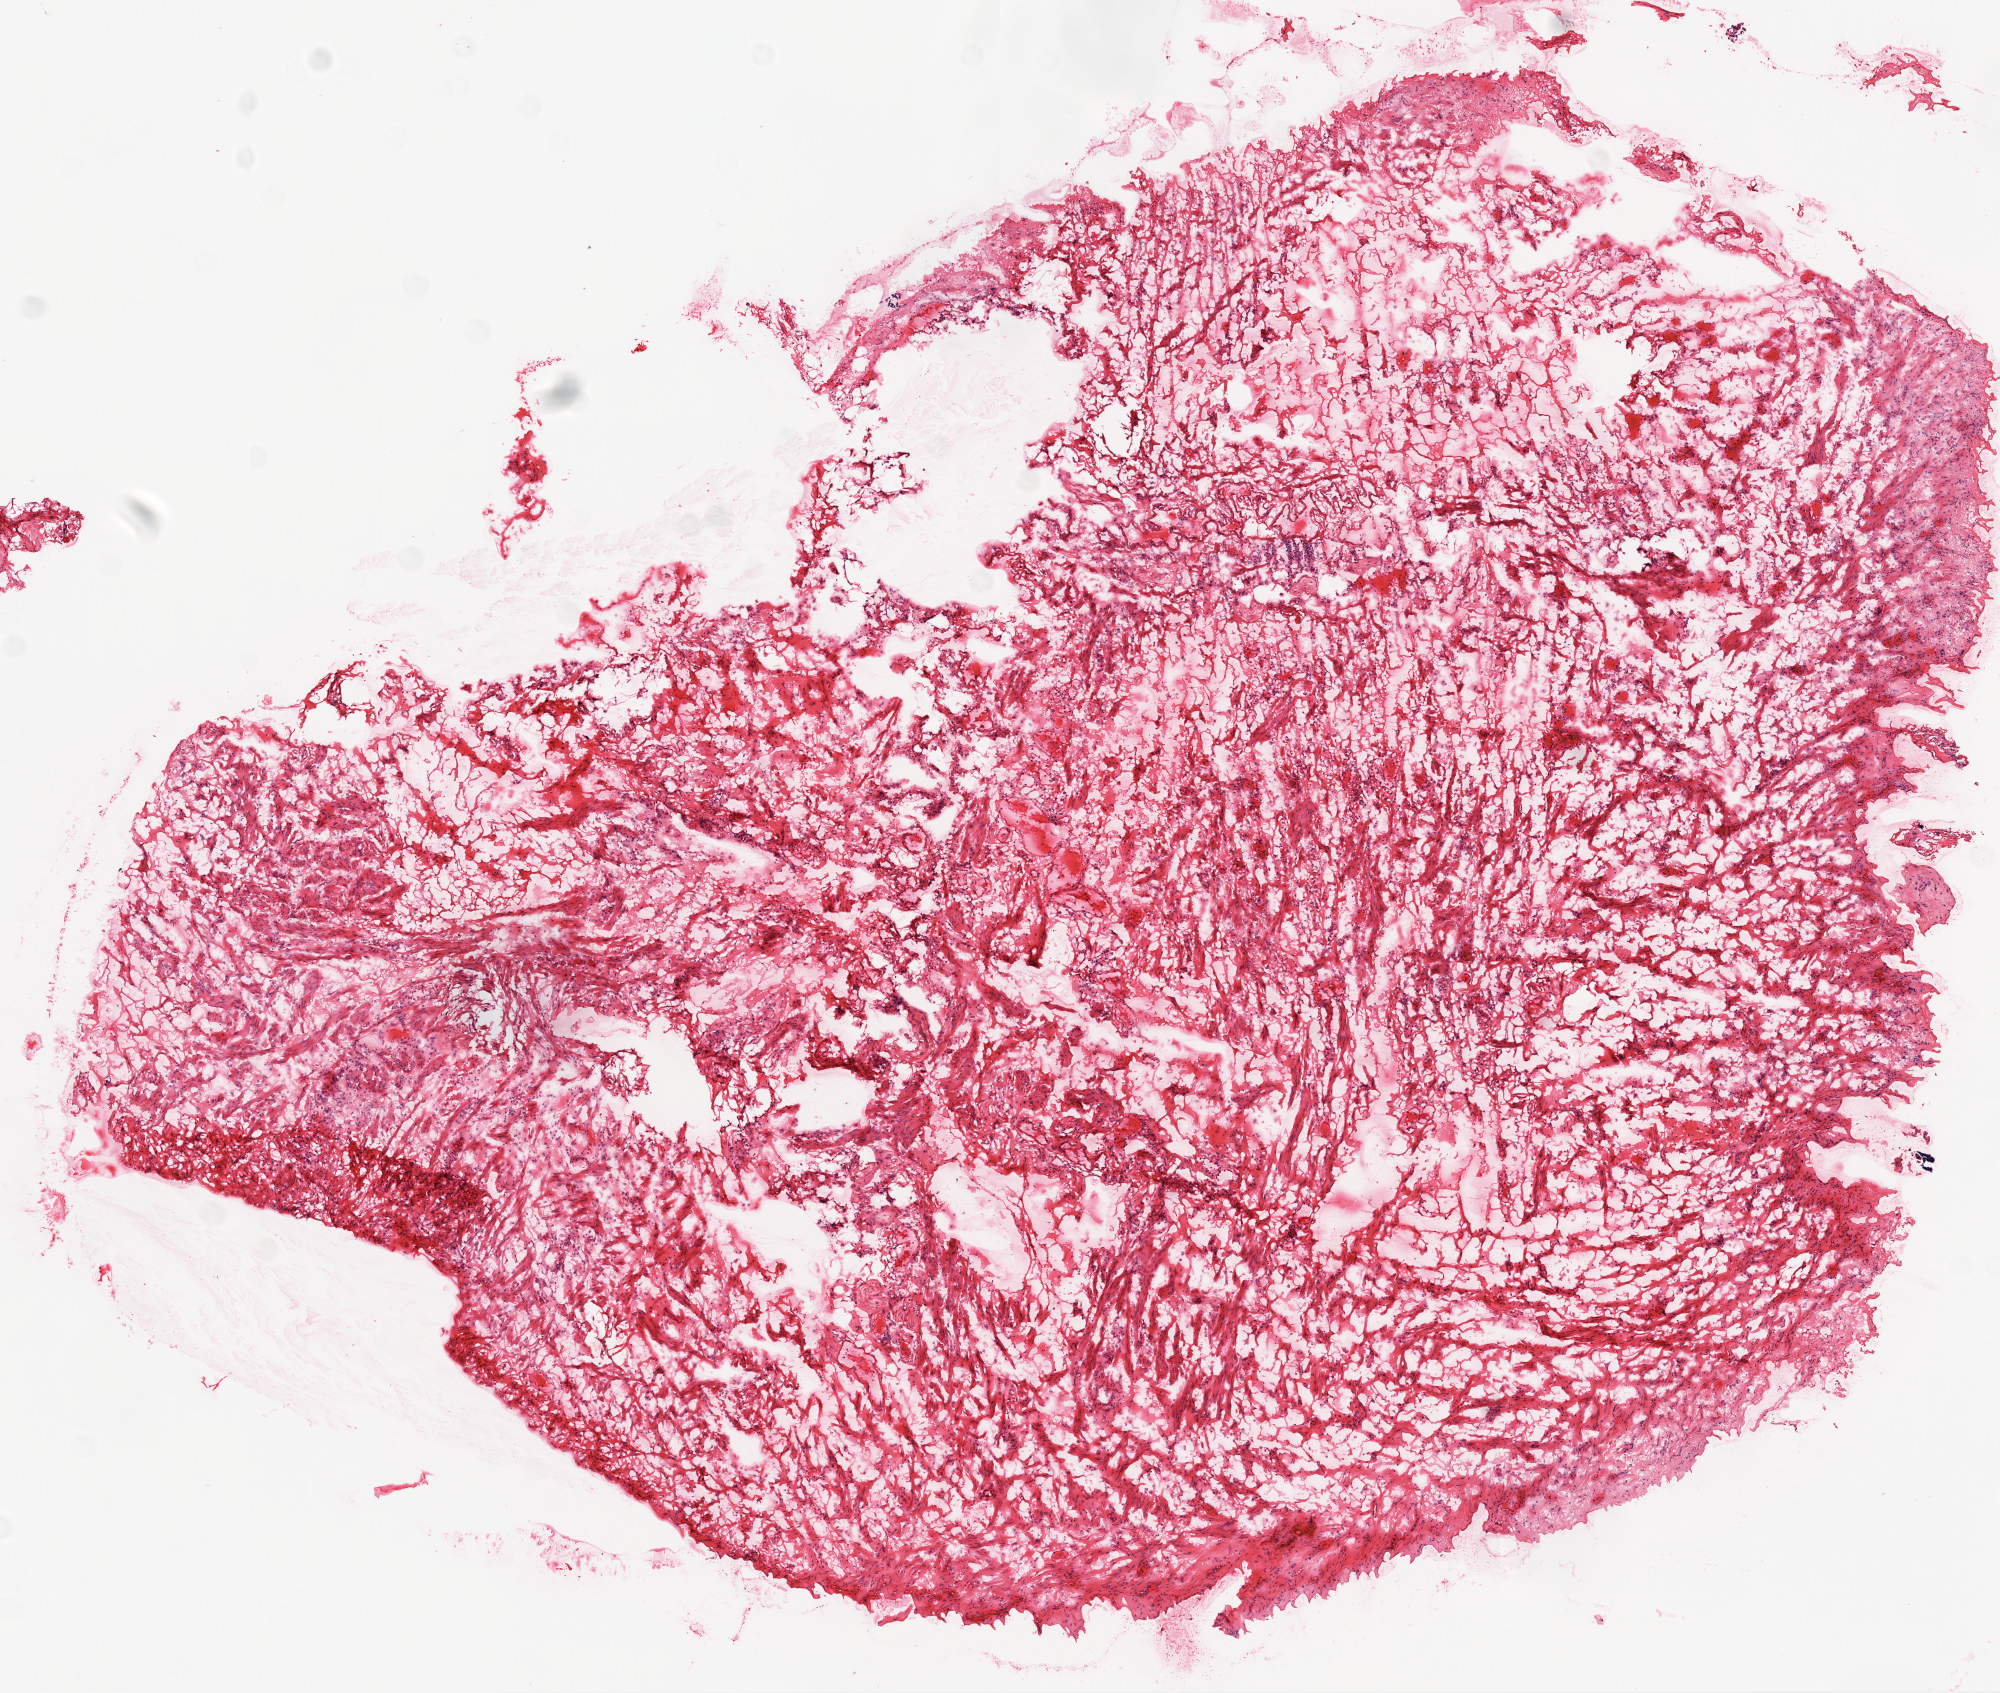
Digitized H&E-stained tissue section (whole slide), low-resolution overview of the scanned area, about 8.0 x 6.8 mm; frozen section from the top of the tissue portion; ovary, solid tissue normal (non-tumour tissue) sample. Female patient; age at initial diagnosis 71 years.
This section: solid tissue normal sample (biorepository sample class). Patient diagnosis: Serous cystadenocarcinoma, NOS.